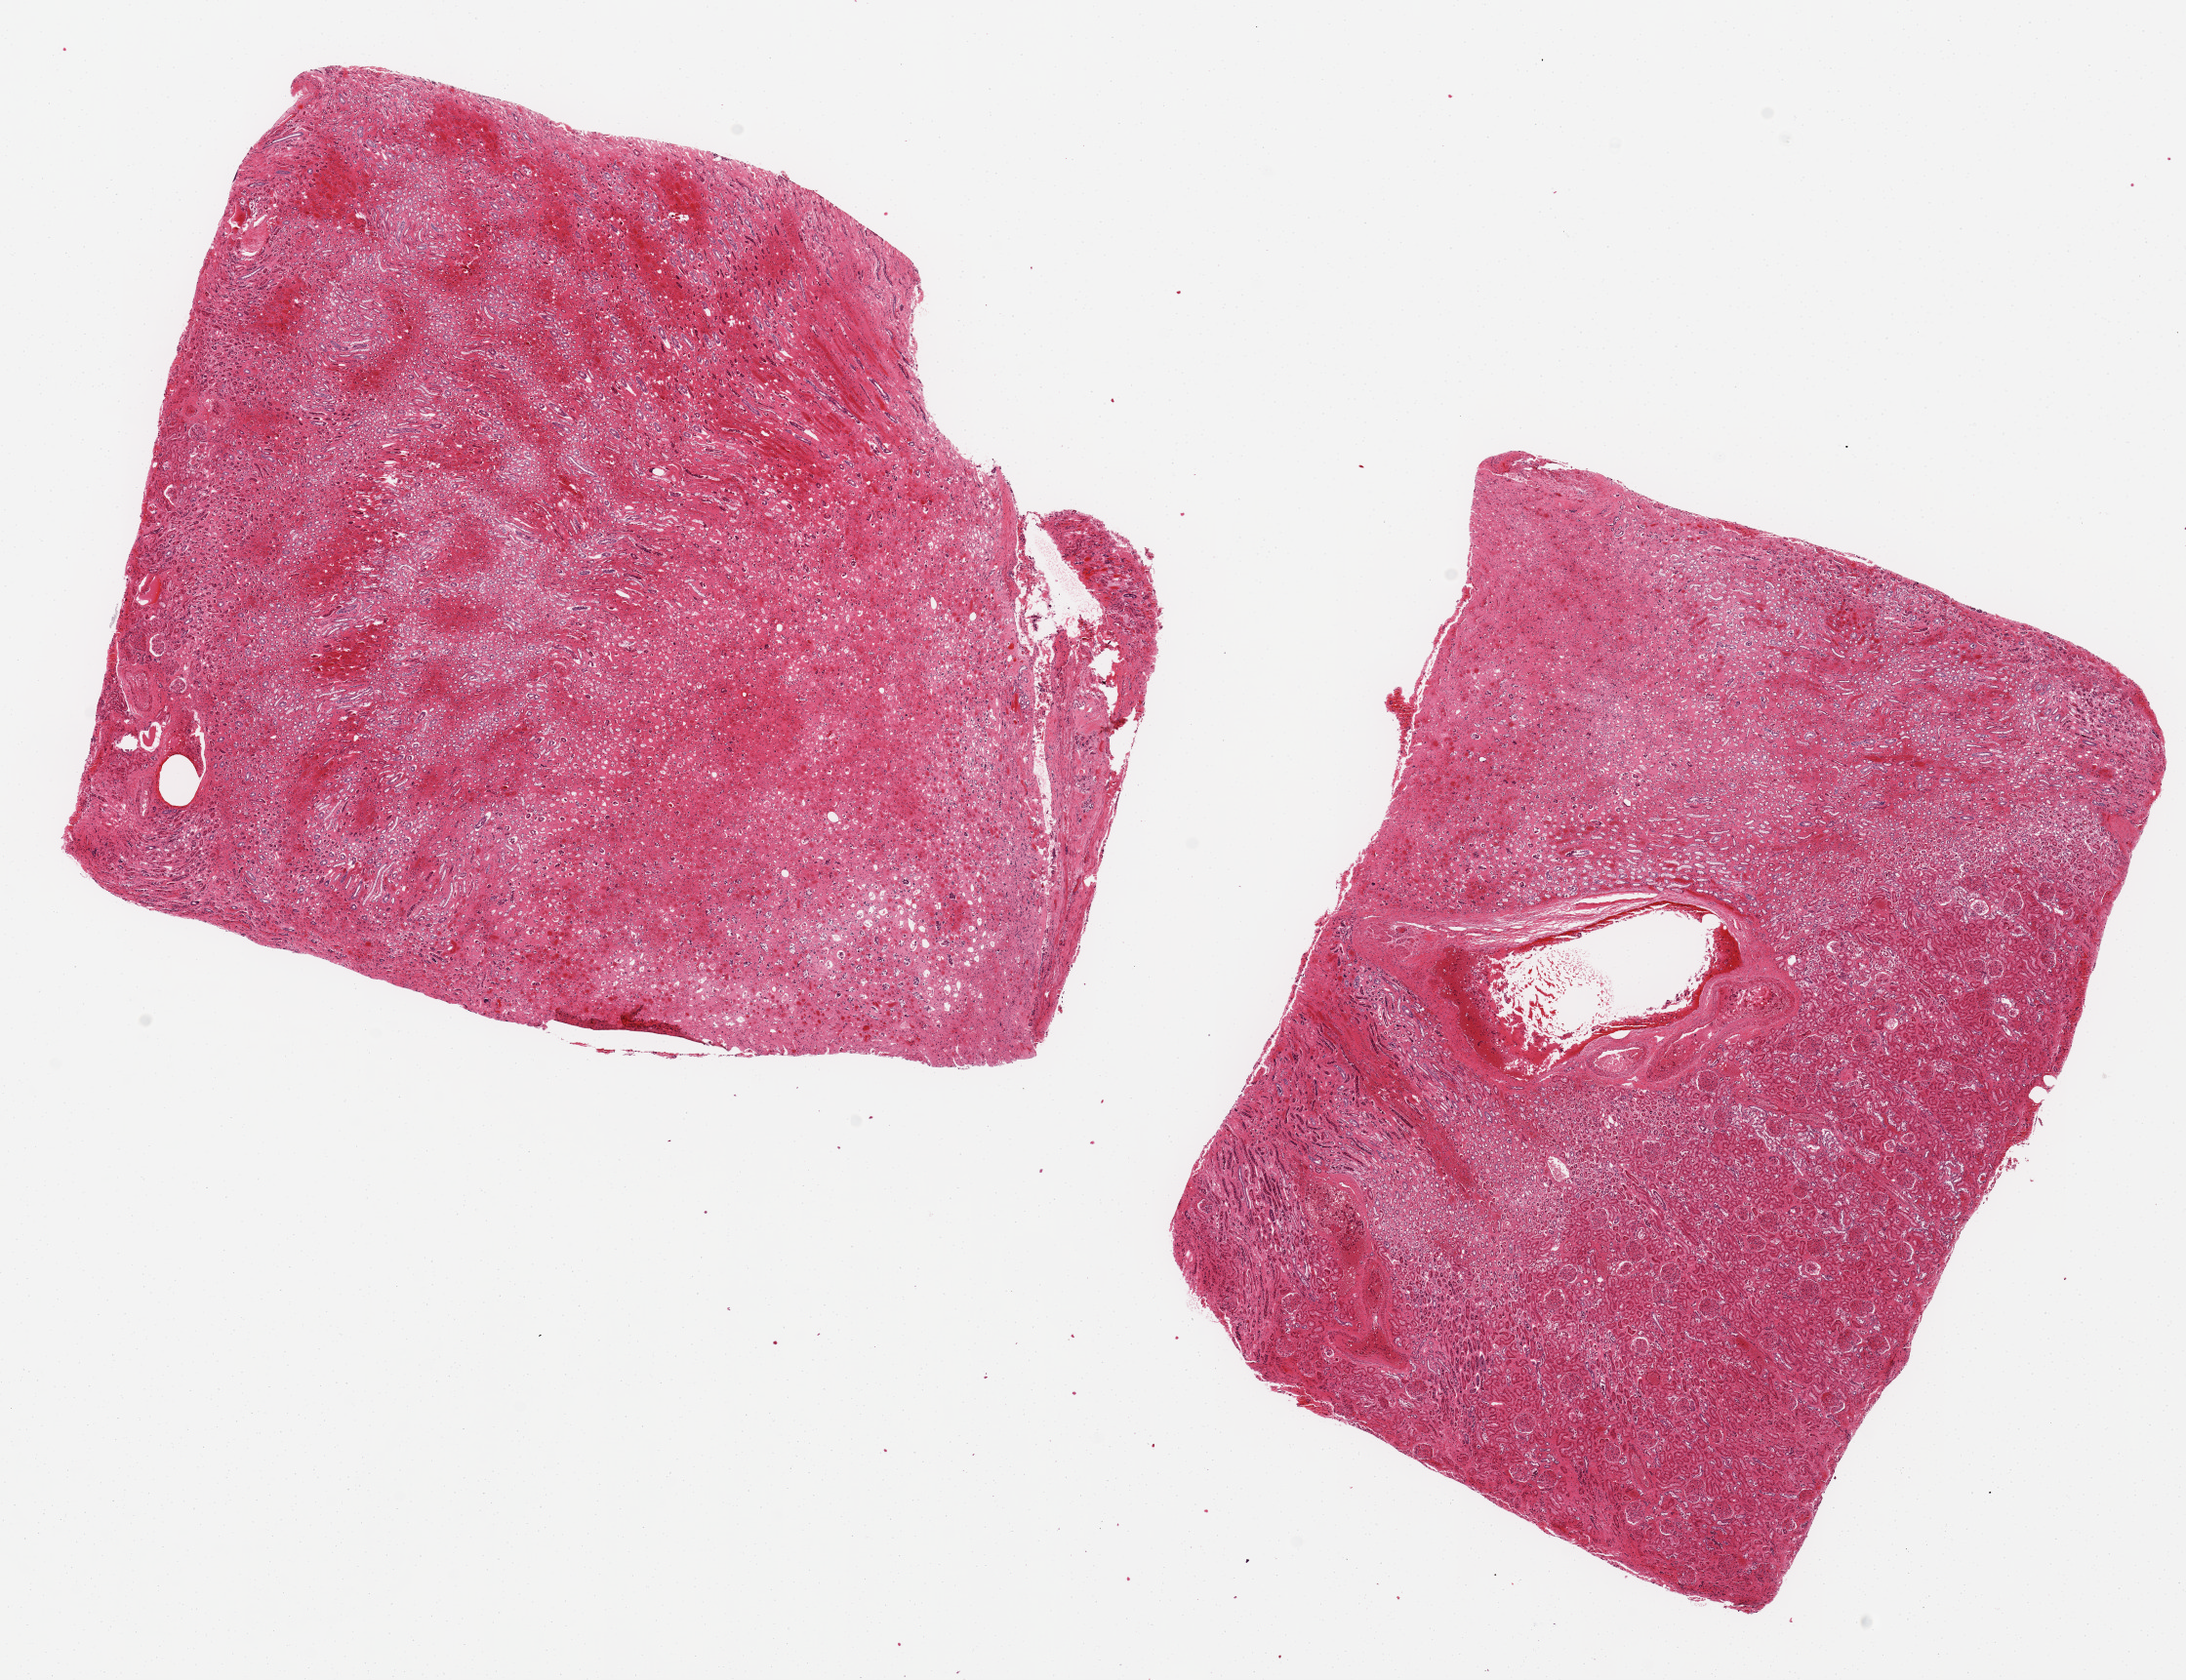
Whole-slide image, hematoxylin and eosin (H&E) stain, brightfield, whole scanned area (about 17.7 x 13.6 mm, slide scanned at 20x) shown as a low-resolution overview. PAXgene-fixed paraffin-embedded (PFPE) section. Sampled site (target tissue): renal medulla. Donor tissue sample. Donor sex: male.
Reviewer comment on this tissue sample: 2 ~7.5x7mm aliquots, one pure tubules (medulla), one ~40% cortex with glomeruli. Tubules badly autolyzed.